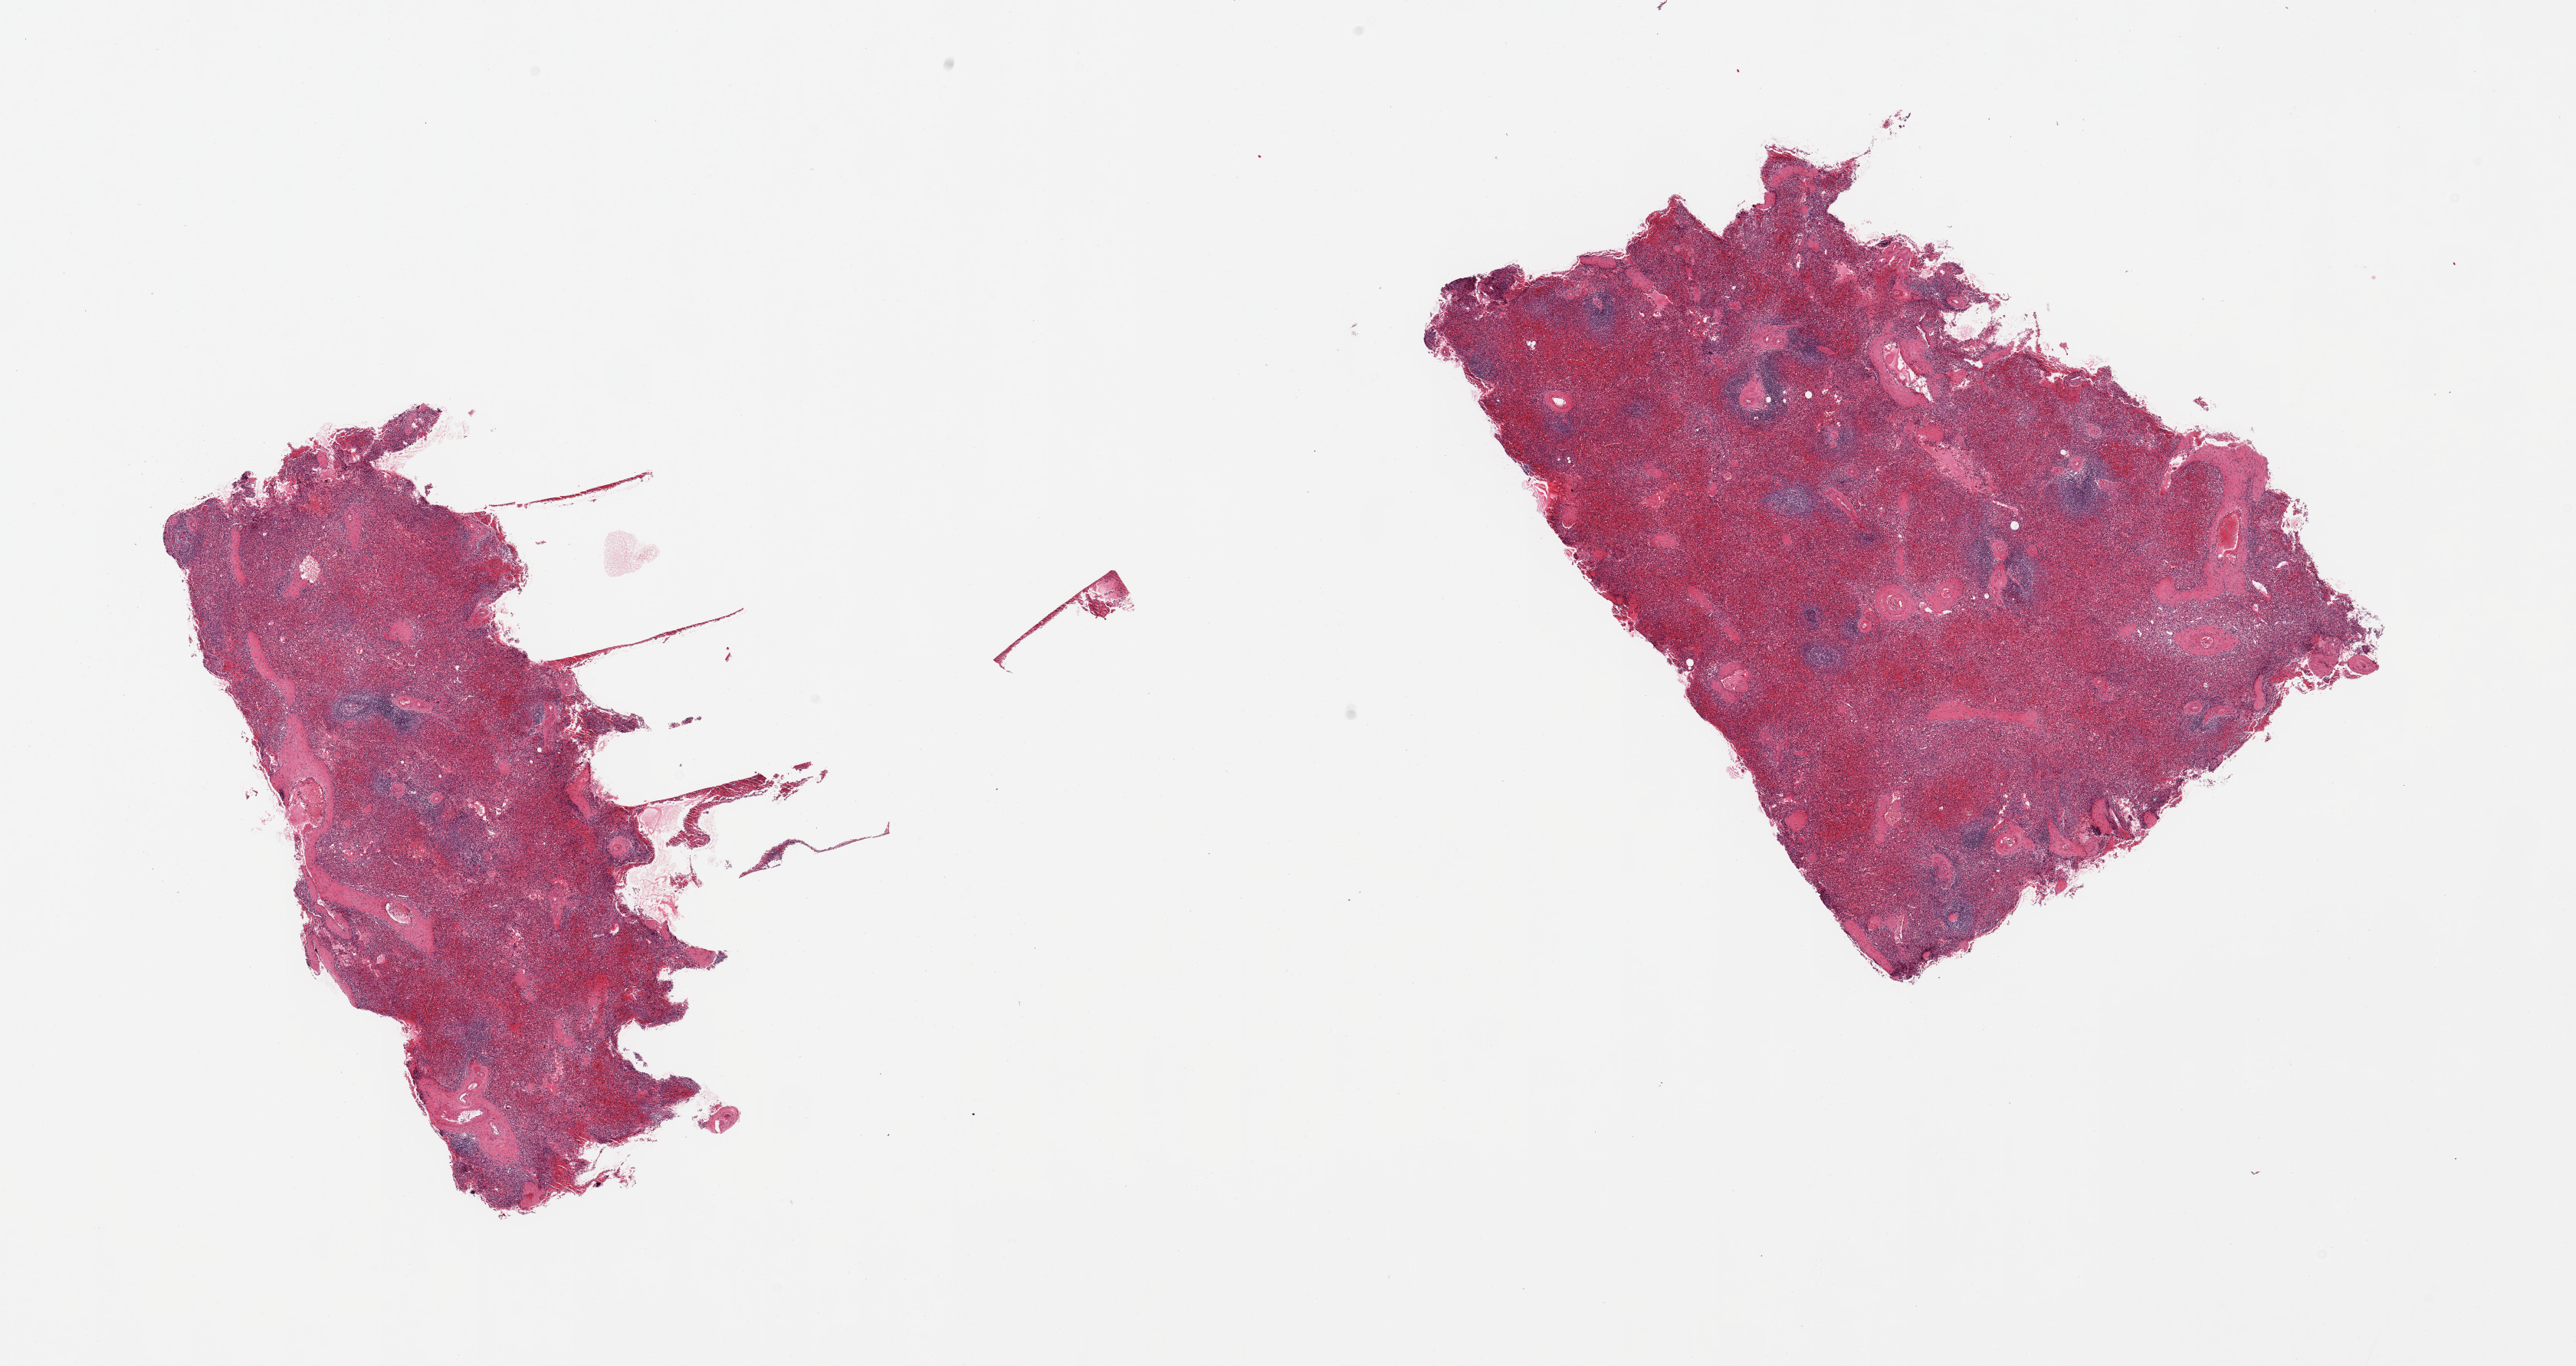
Whole-slide image, haematoxylin and eosin stain — whole scanned area (about 26.6 x 14.1 mm, acquisition: 20x scan) shown as a low-resolution overview, PAXgene-fixed paraffin-embedded (PFPE) section, sampled site (target tissue): spleen, donor tissue sample.
- reviewer comment on this tissue sample: 2 pieces; congested